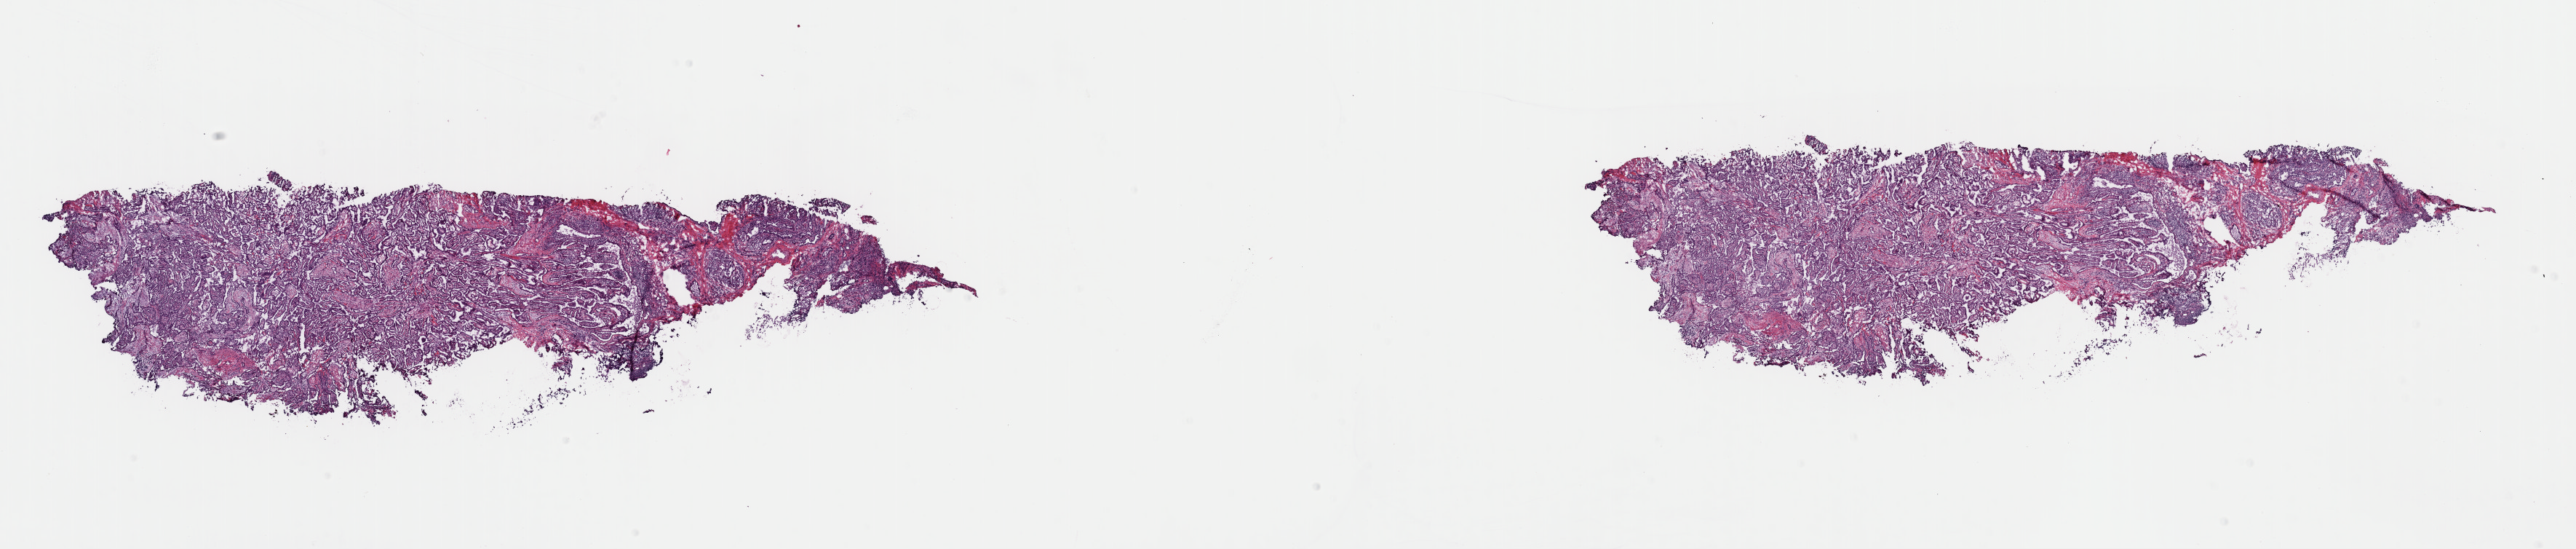
Whole-slide histology image, Hematoxylin and eosin (H&E) stained — shown as a low-resolution overview of the whole scanned area (about 28.0 x 6.0 mm, slide scanned at 40x), frozen section, primary tumour sample from the thyroid. Patient: female, age at initial diagnosis 32 years. Composition of this section per pathologist review: tumour cells 75%, tumour nuclei 75%, normal cells 0%, stromal cells 25%, necrosis 0%. Inflammatory infiltration, as recorded: lymphocyte infiltration 7%, monocyte infiltration 0%, neutrophil infiltration 0%.
AJCC pathologic stage: I (7th edition). Lymph nodes positive (case pathology): 6 of 14 examined. TNM: T1b N1a M0. Laterality: midline. Histologic diagnosis: Papillary adenocarcinoma, NOS (thyroid gland).